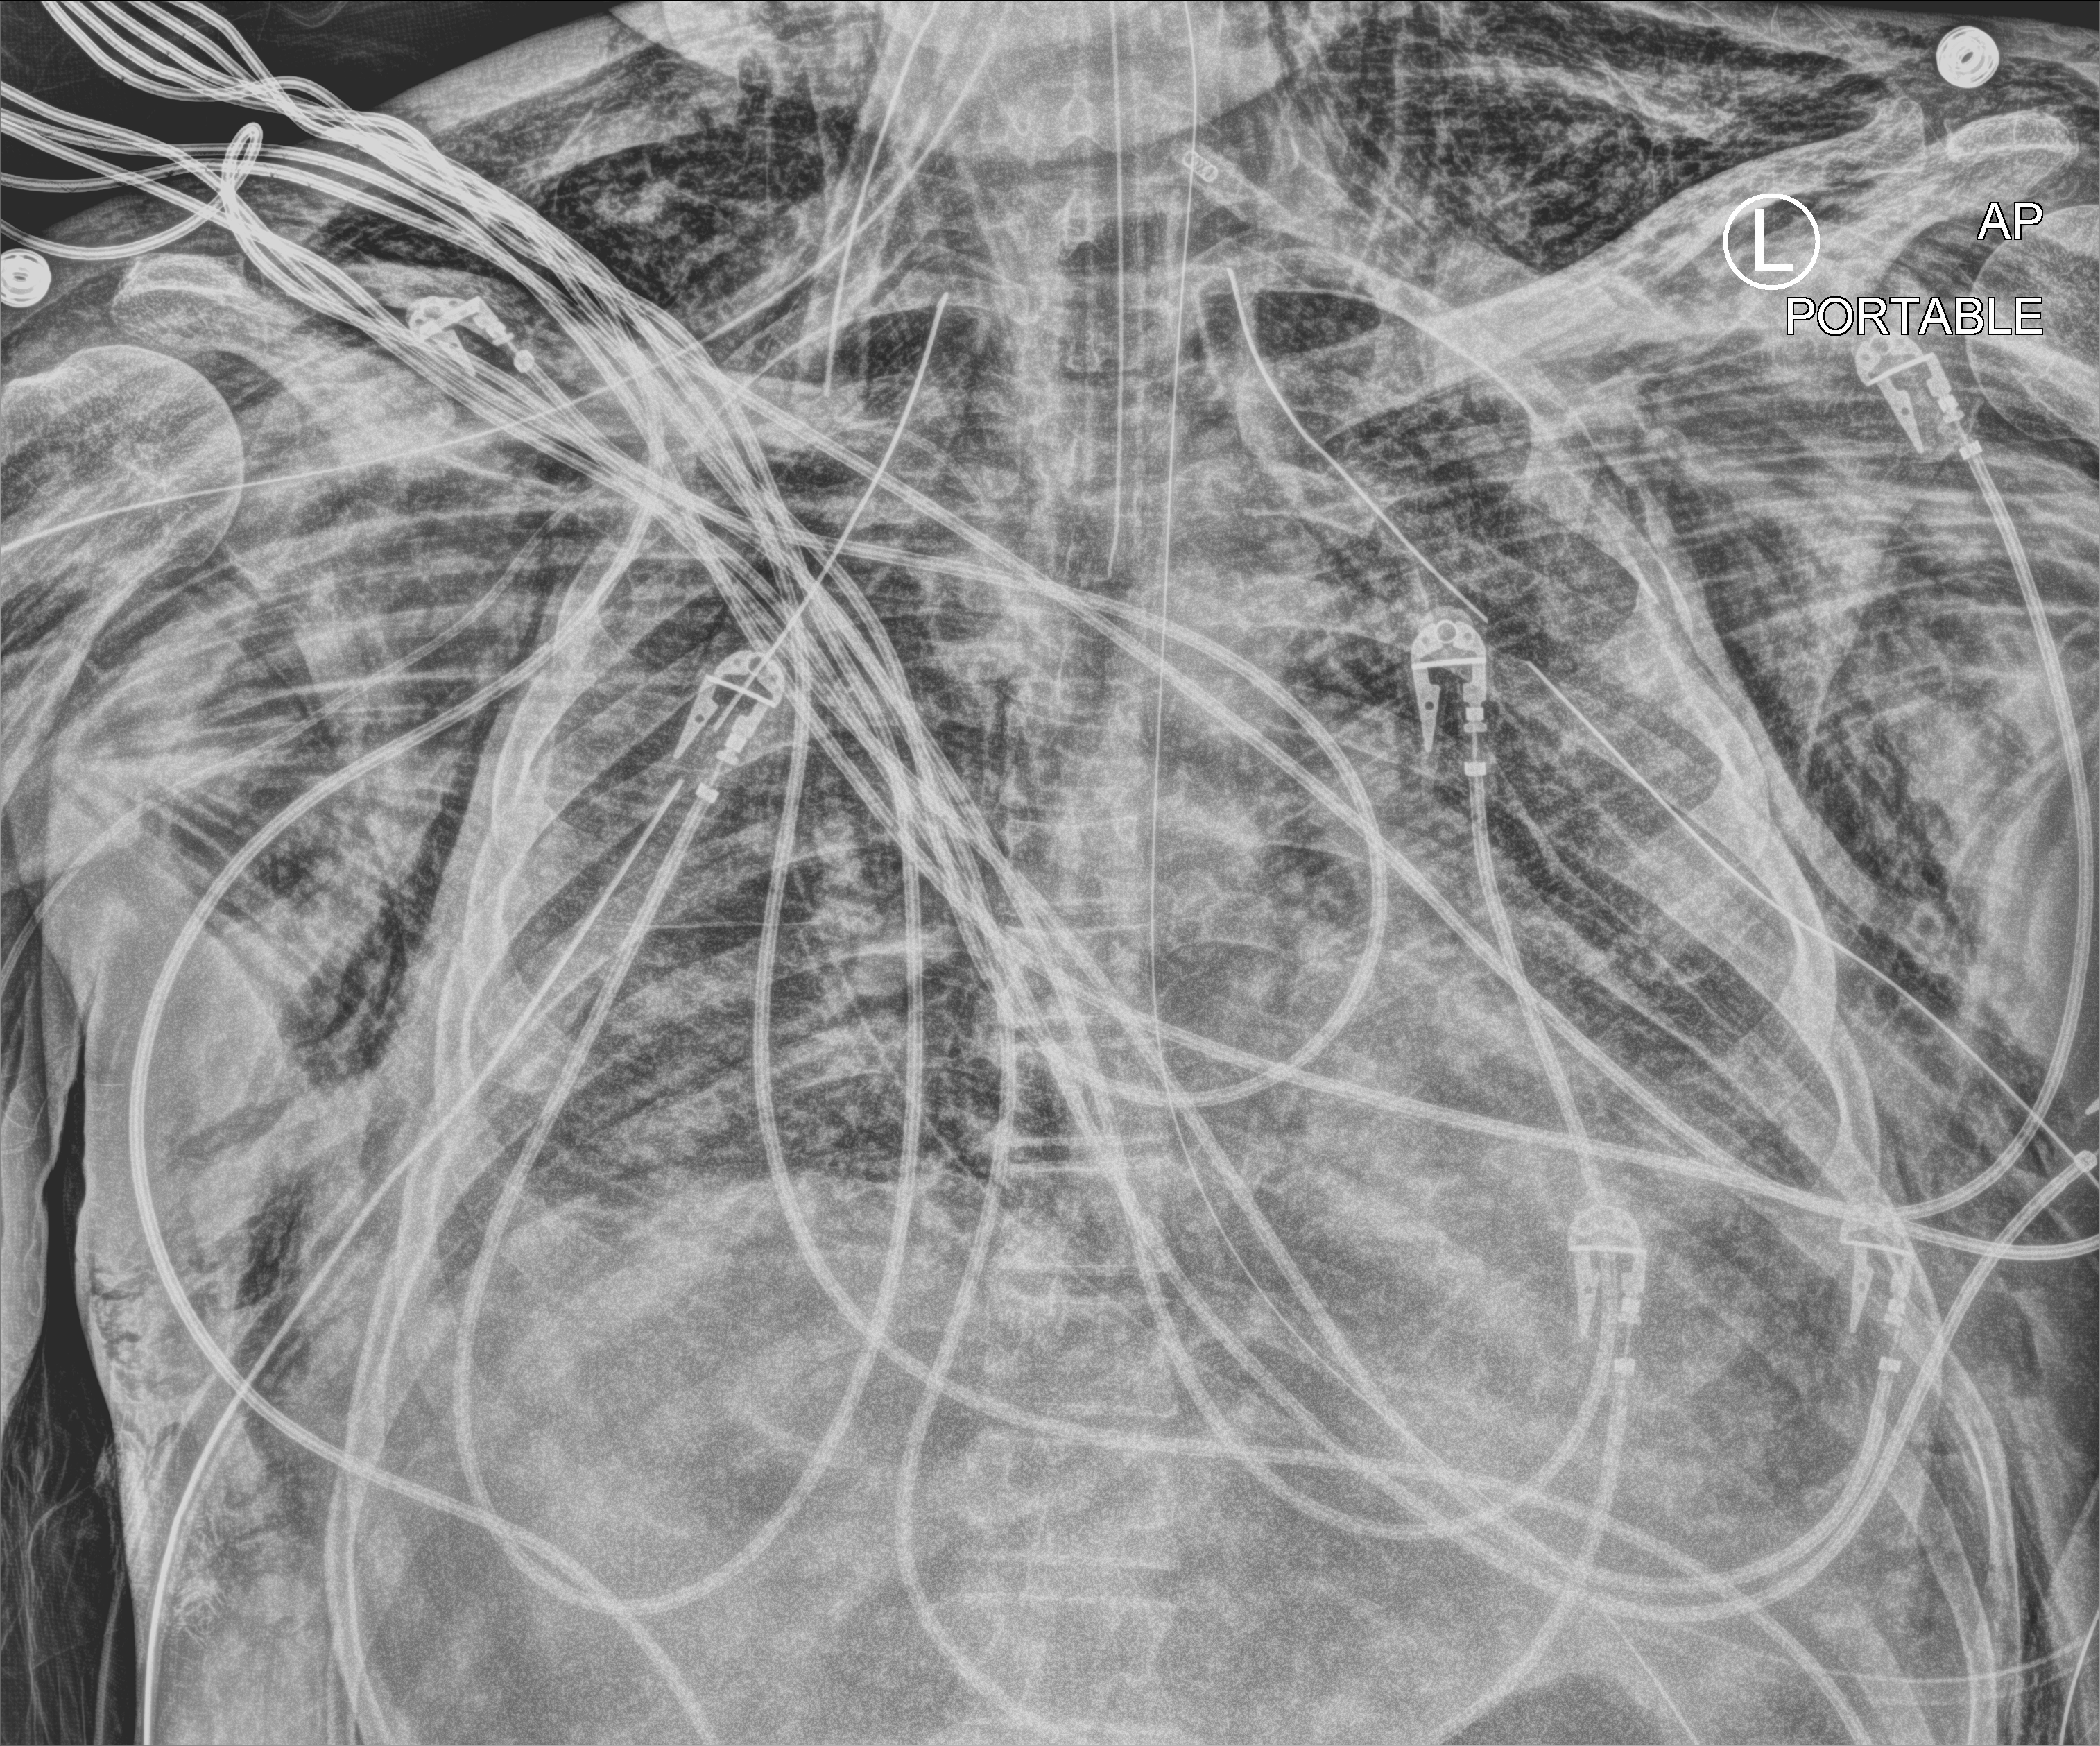
Bedside chest radiograph (computed radiography). Male patient hospitalised with COVID-19, age 18–59 years.
From the hospital-stay record, not from the radiograph (when in the stay this image was taken is not recorded): length of hospital stay: 83 days; hypertension (admission record): yes; mechanically ventilated during this hospital stay: yes.